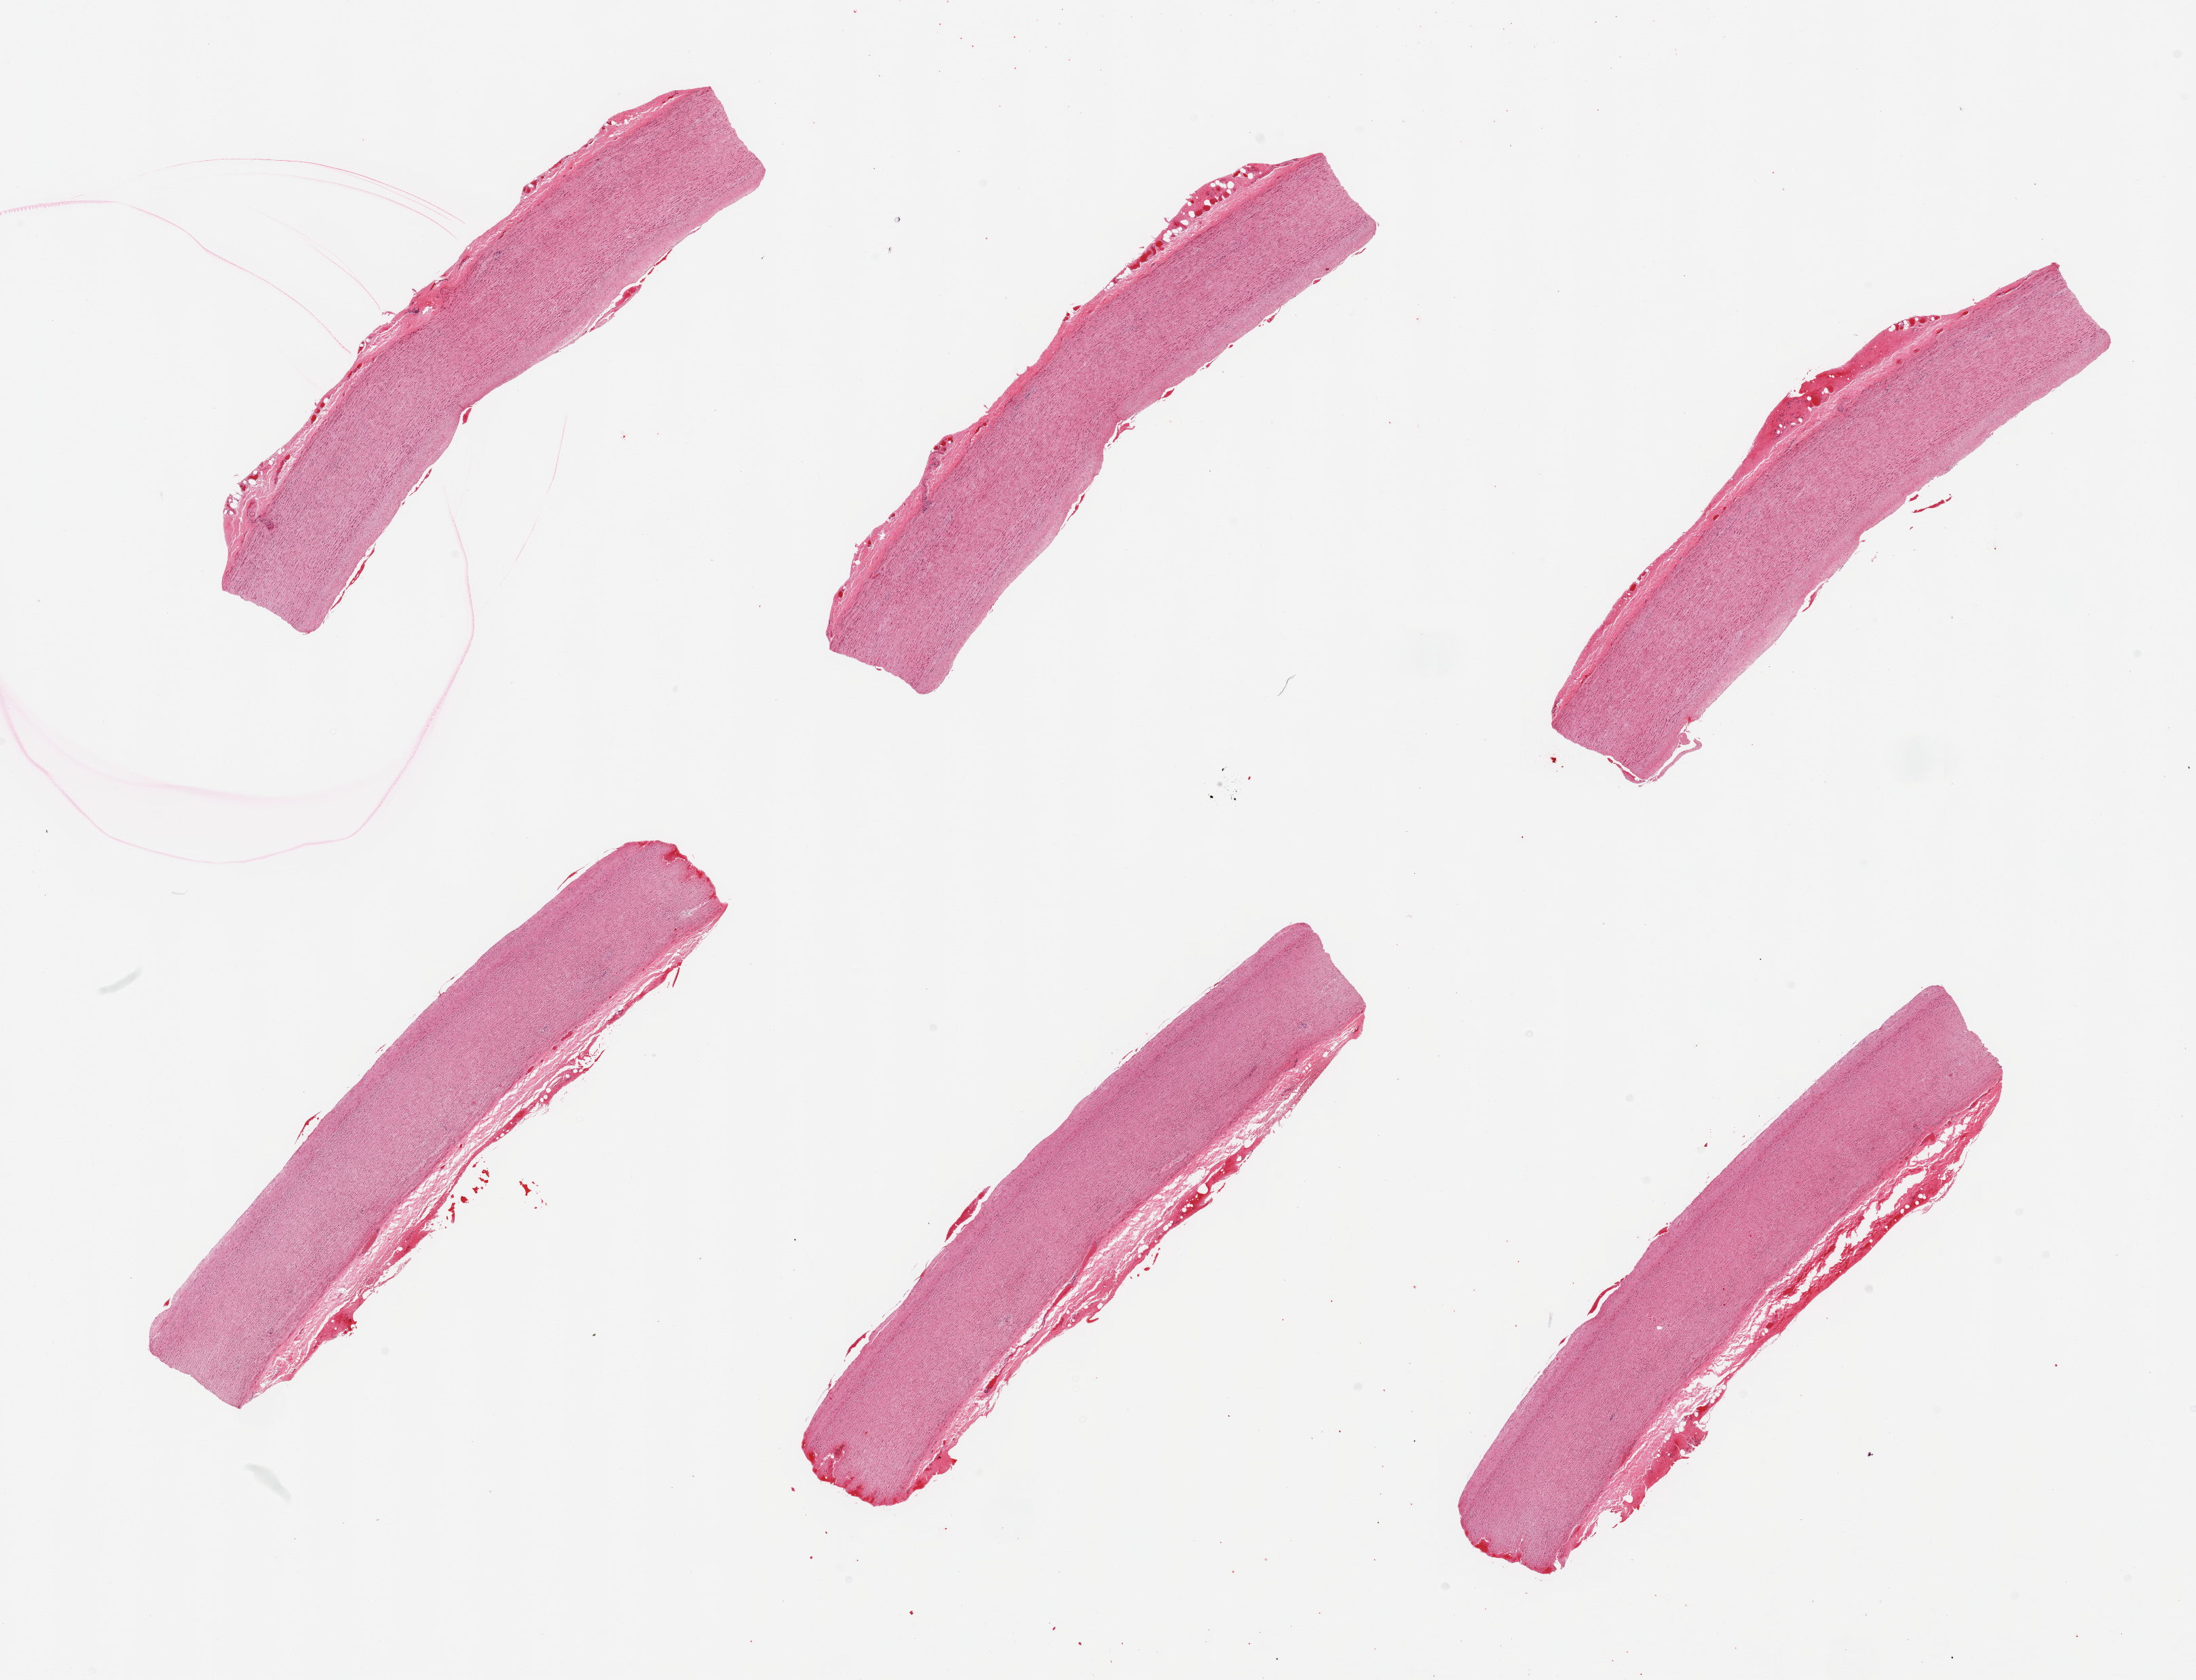
Digitized haematoxylin and eosin-stained section, a low-resolution overview of the entire scanned area, about 25.6 x 19.6 mm (slide scanned at 20x), PAXgene-fixed, paraffin-embedded tissue, sampled site (target tissue): aorta, donor tissue sample. Donor: male.
Reviewer comment on this tissue sample: 6 pieces; early flat atheromatous plaque; sparse rim of congested adventitia.